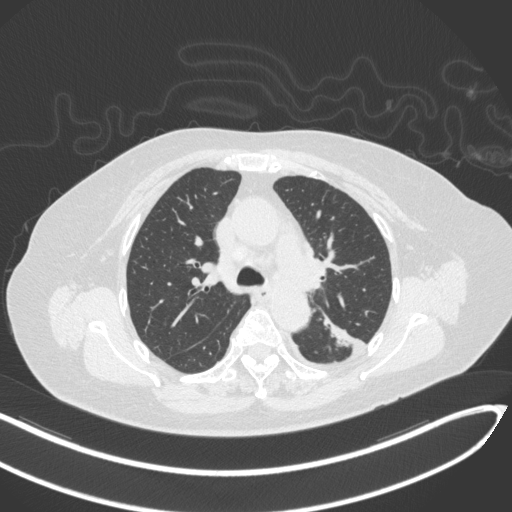
Chest CT, one axial slice; position 212 of 270 along the scan axis; reconstruction kernel B31f; 120 kVp; lung window (W 1500 / L -600 HU); 512 × 512 image matrix, field of view 400 × 400 mm. Female patient, age 76 years. Case-level facts recorded for this patient, not image findings: clinical TNM (as recorded): T1c N0 M0.
Outlined on this slice (bounding box drawn by a radiologist):
- lung tumour (recorded histology: adenocarcinoma): box from (x=326, y=321) to (x=362, y=356) px